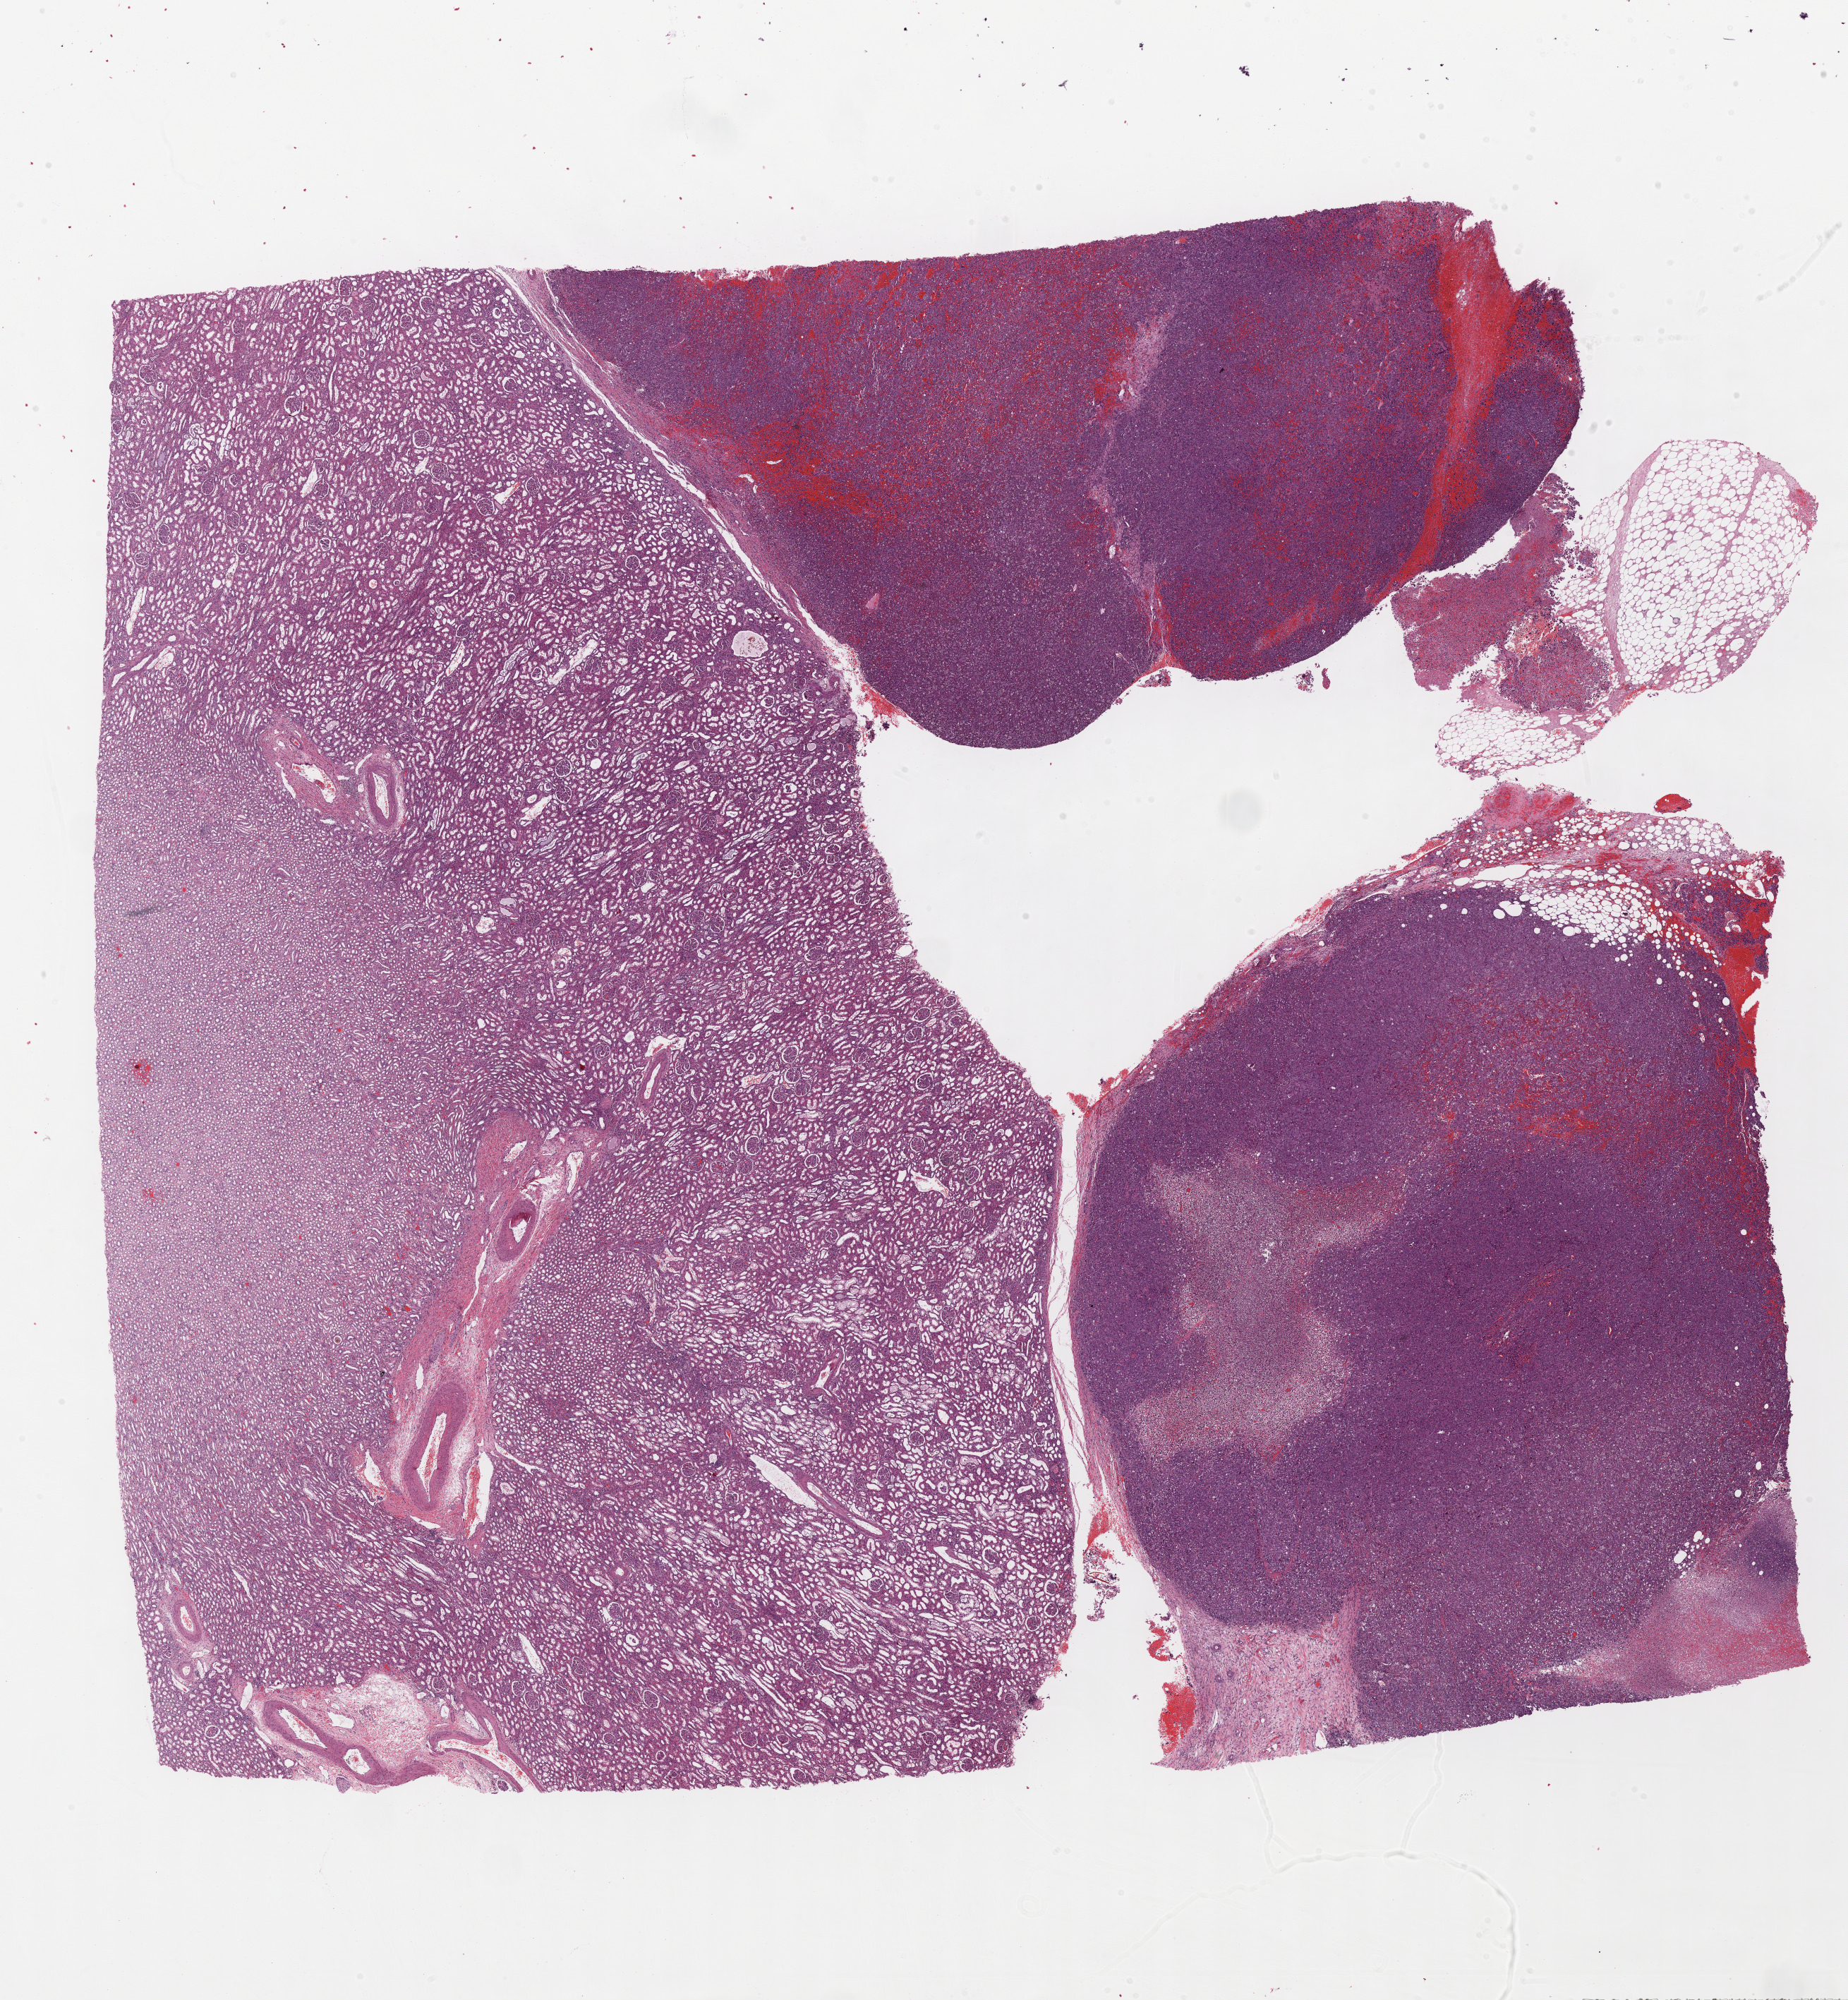
Hematoxylin and eosin (H&E) stained whole-slide image, a low-resolution overview of the entire scanned area, about 21.1 x 22.9 mm (slide scanned at 20x), formalin-fixed paraffin-embedded (FFPE) diagnostic section, adrenal cortex, primary tumour sample. Female, age 45 years at initial diagnosis.
Histologic diagnosis: Adrenal cortical carcinoma (cortex of adrenal gland). Lymph nodes positive (case pathology): 0 of 6 examined.